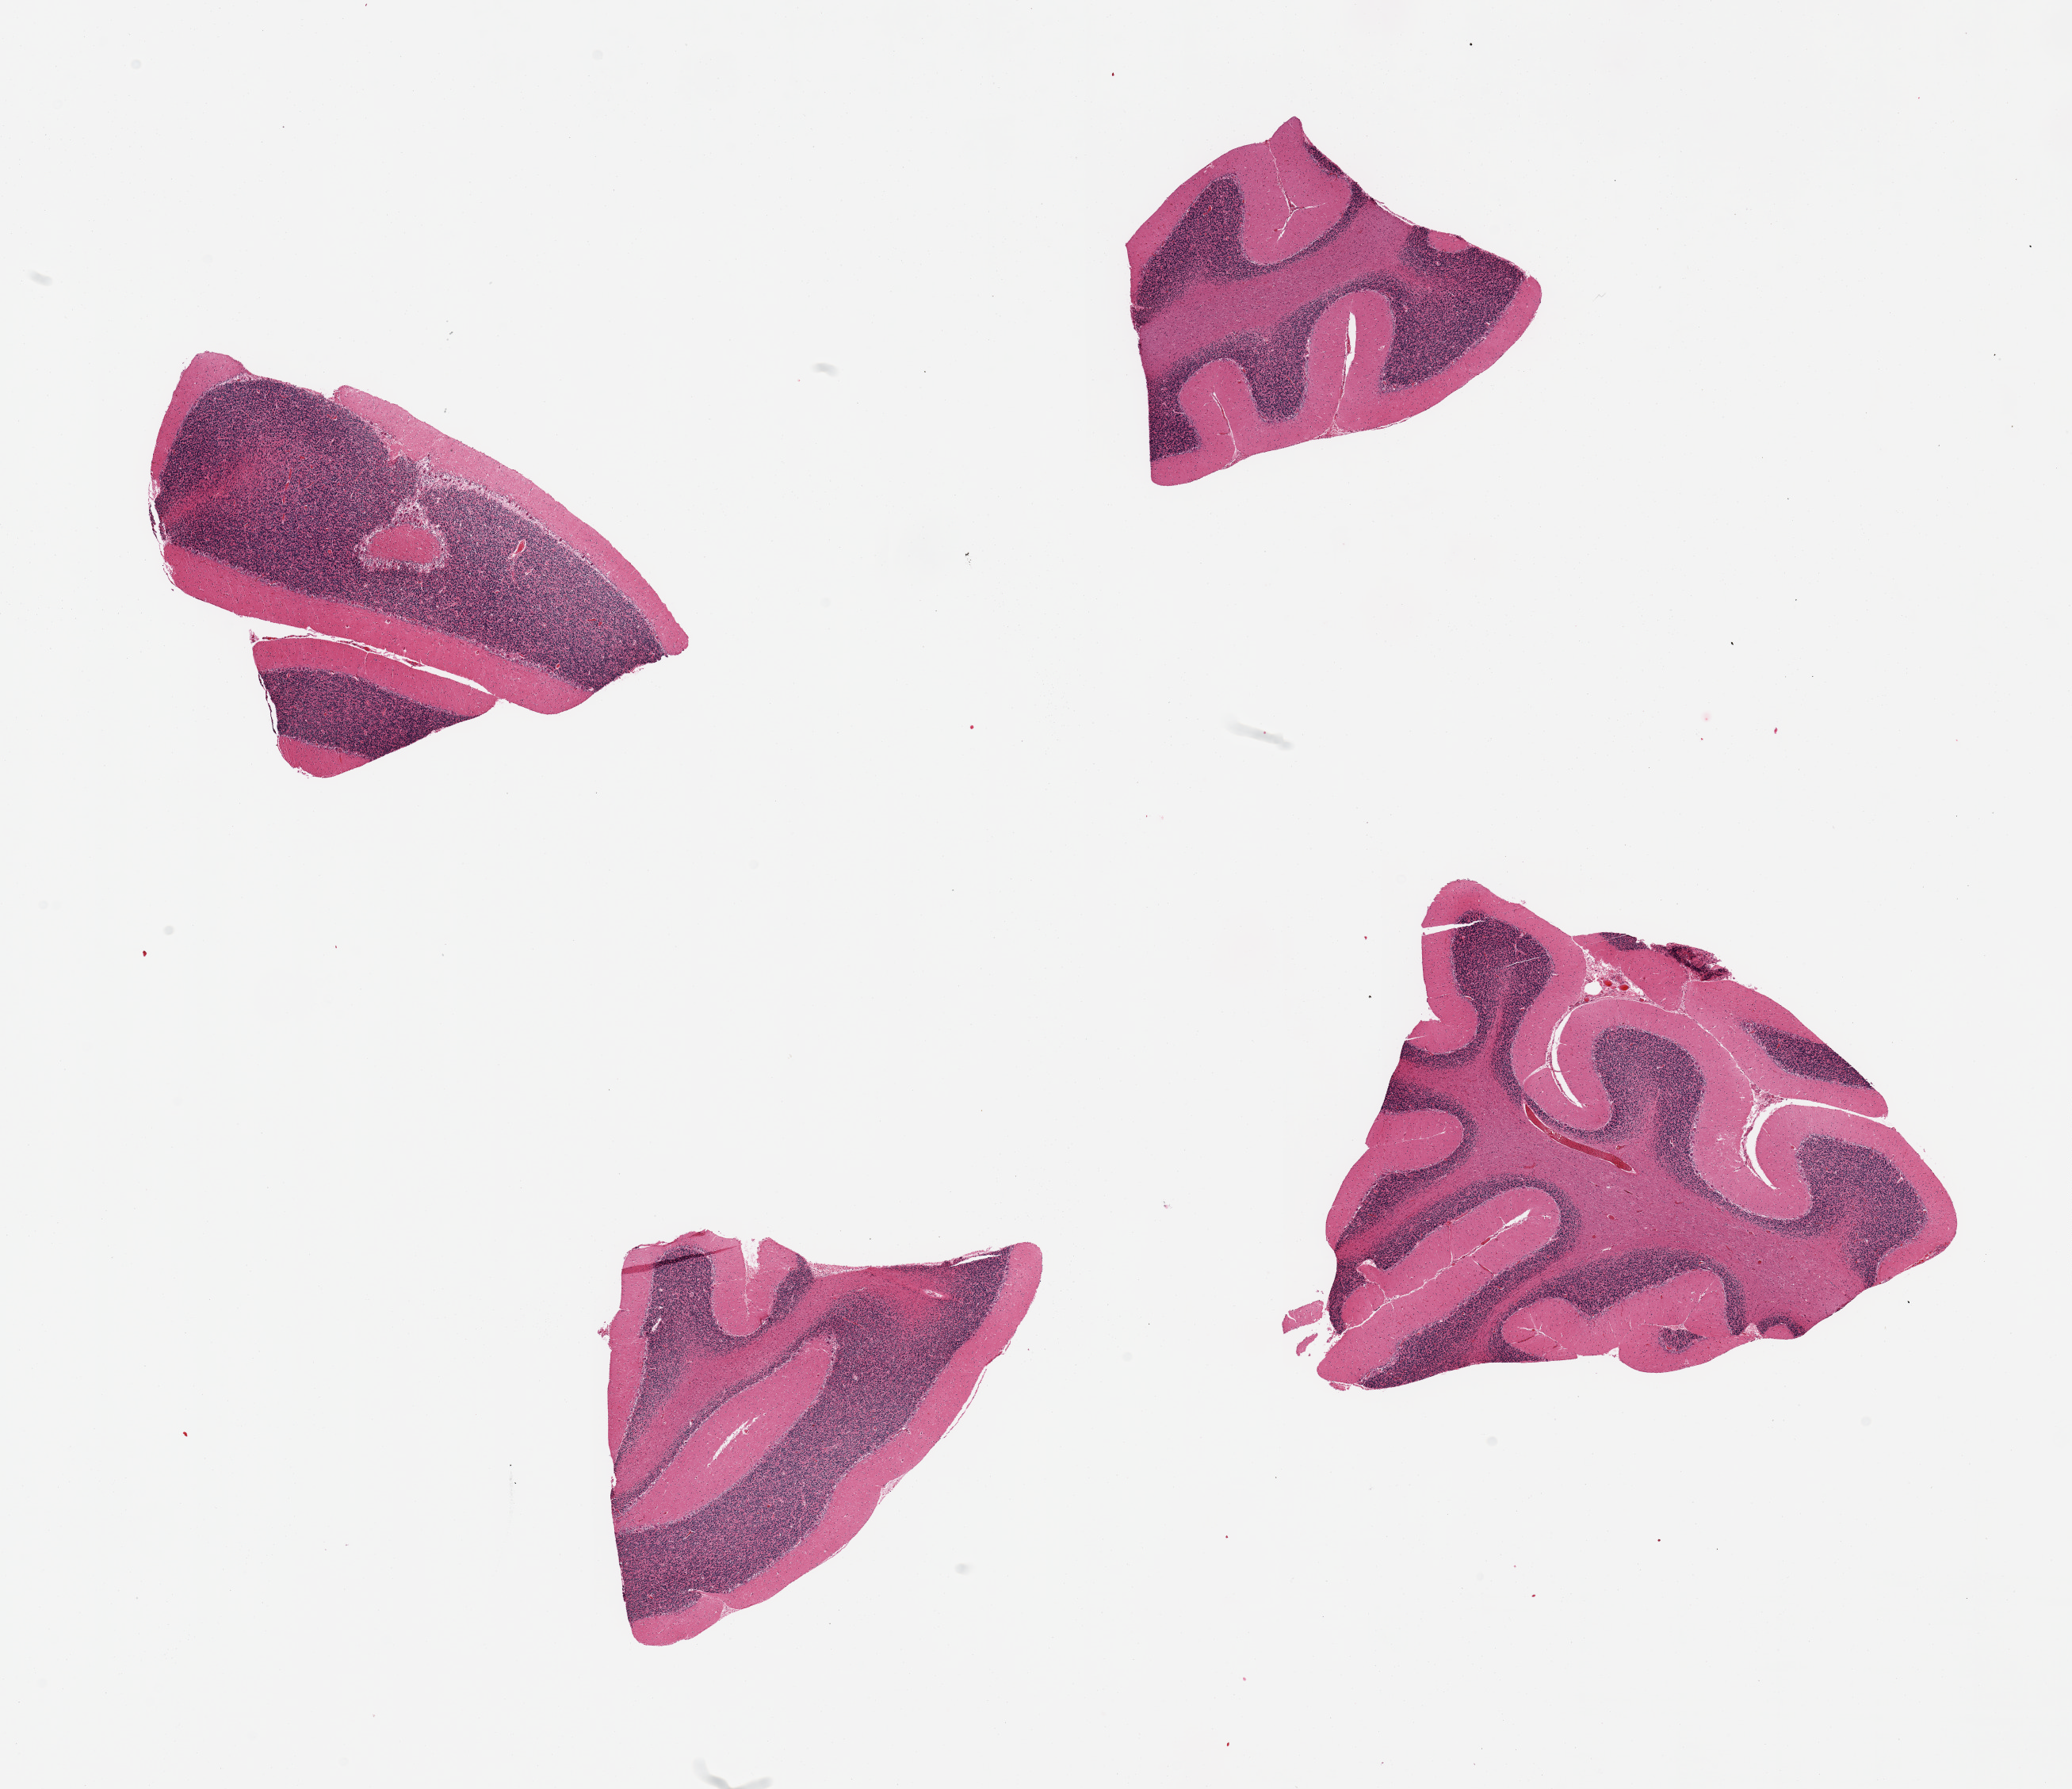
Digitized haematoxylin and eosin-stained section, a low-resolution overview of the entire scanned area, about 20.7 x 17.8 mm (acquisition: 20x scan); PAXgene-fixed, paraffin-embedded tissue; section of cerebellum (target tissue); donor tissue sample. Donor: female.
Reviewer comment on this tissue sample: 4 pieces, no abnormalities.